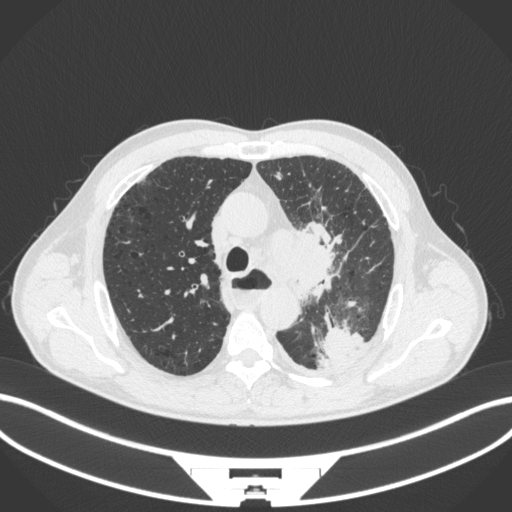
Chest CT, one axial slice; reconstruction kernel B31f; 120 kVp; lung window (W 1500 / L -600 HU); 1 mm slice thickness; 512 × 512 image matrix, field of view 400 × 400 mm. Male patient, age 57 years. Case-level facts recorded for this patient, not image findings: clinical TNM (as recorded): T2a N1 M0.
Structures marked on this image (bounding box drawn by a radiologist):
- lung tumour (recorded histology: squamous cell carcinoma): box from (x=264, y=225) to (x=345, y=294) px